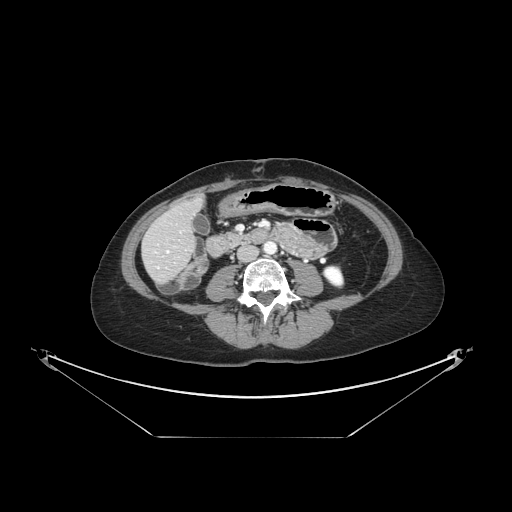
Contrast-enhanced abdominal CT, one axial slice; slice 35 of 148 in the series (ordered by position); reconstruction kernel STANDARD; 120 kVp; intravenous contrast given; soft-tissue window (W 400 / L 40 HU); 2.5 mm slice thickness; 512 × 512 image matrix, field of view 500 × 500 mm. Female patient, age 73 years. From the clinical record (not read from this slice): diagnosis: colorectal cancer liver metastases, imaged before liver resection; multiple liver metastases: no; largest metastasis: 1 cm; disease in both lobes: no.
Structures marked on this image (expert manual segmentation):
- liver: bounding box (x1, y1, x2, y2) in pixels: (144, 201, 200, 282)
- planned liver remnant (the part of the liver to remain after resection): (162, 201, 200, 239)